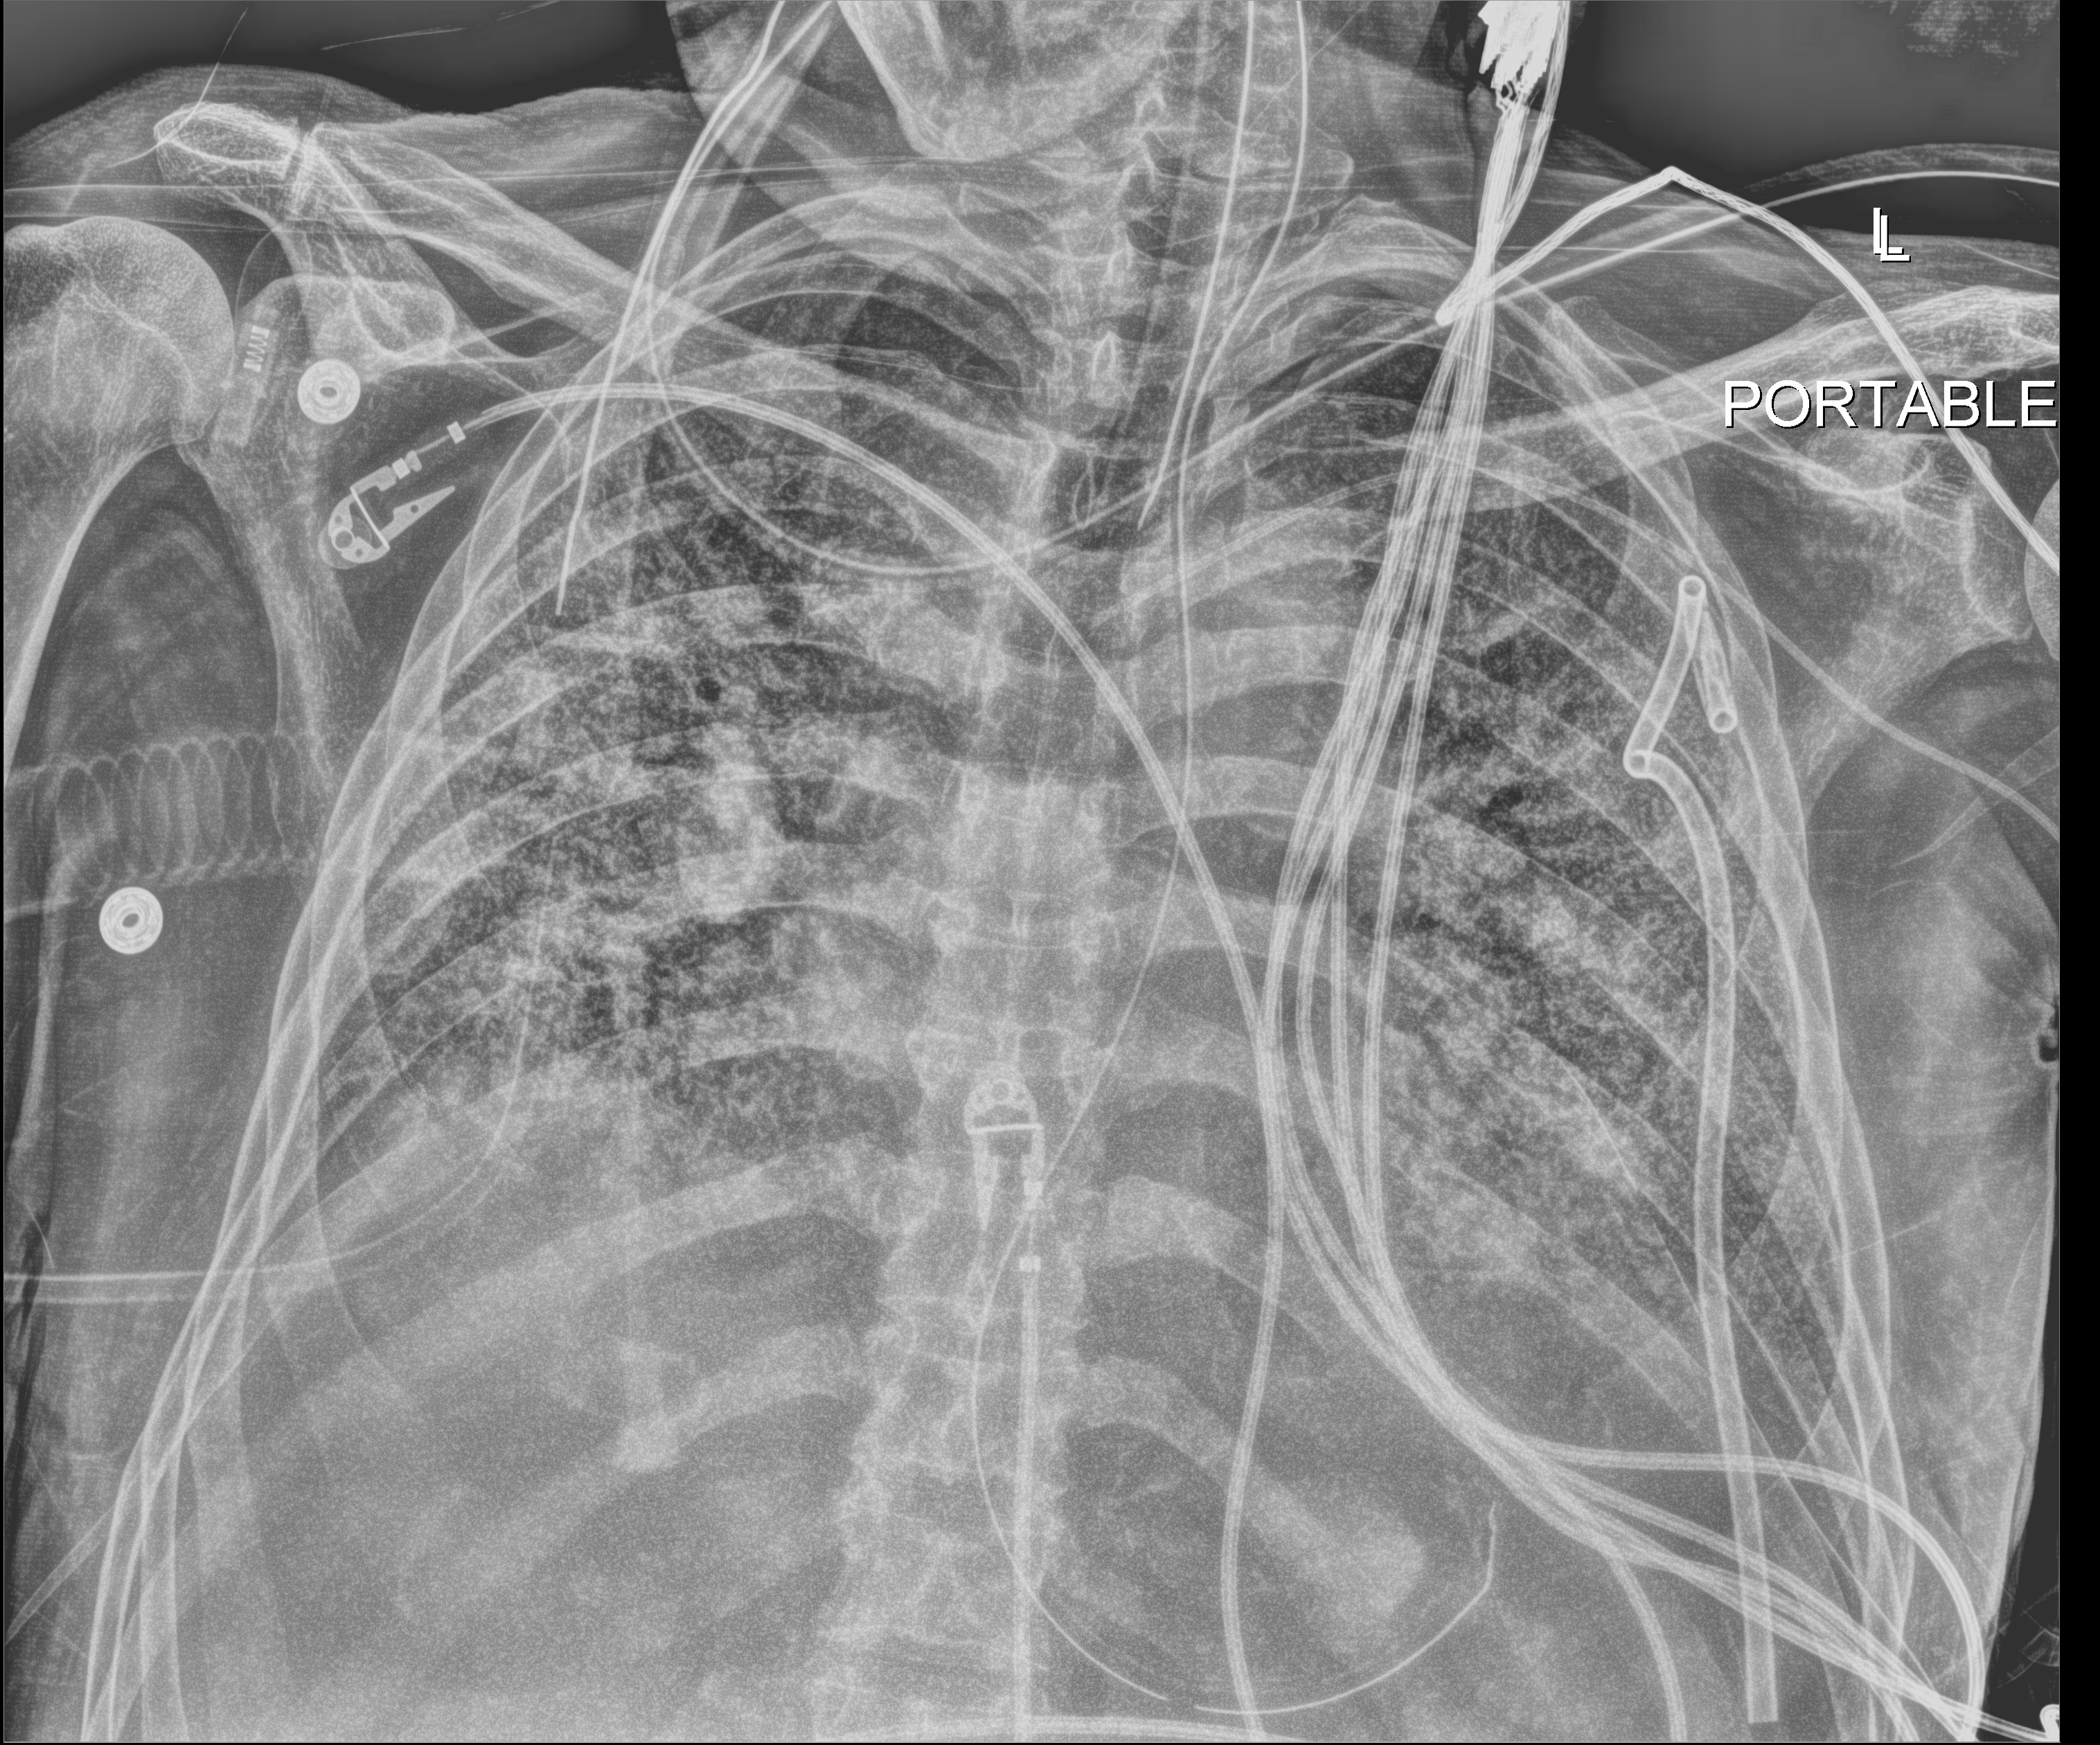
Chest X-ray (portable), anteroposterior (AP) projection. Patient hospitalised with COVID-19; male, aged 60–74 years.
From the hospital-stay record, not from the radiograph (when in the stay this image was taken is not recorded):
- mechanically ventilated during this hospital stay: yes